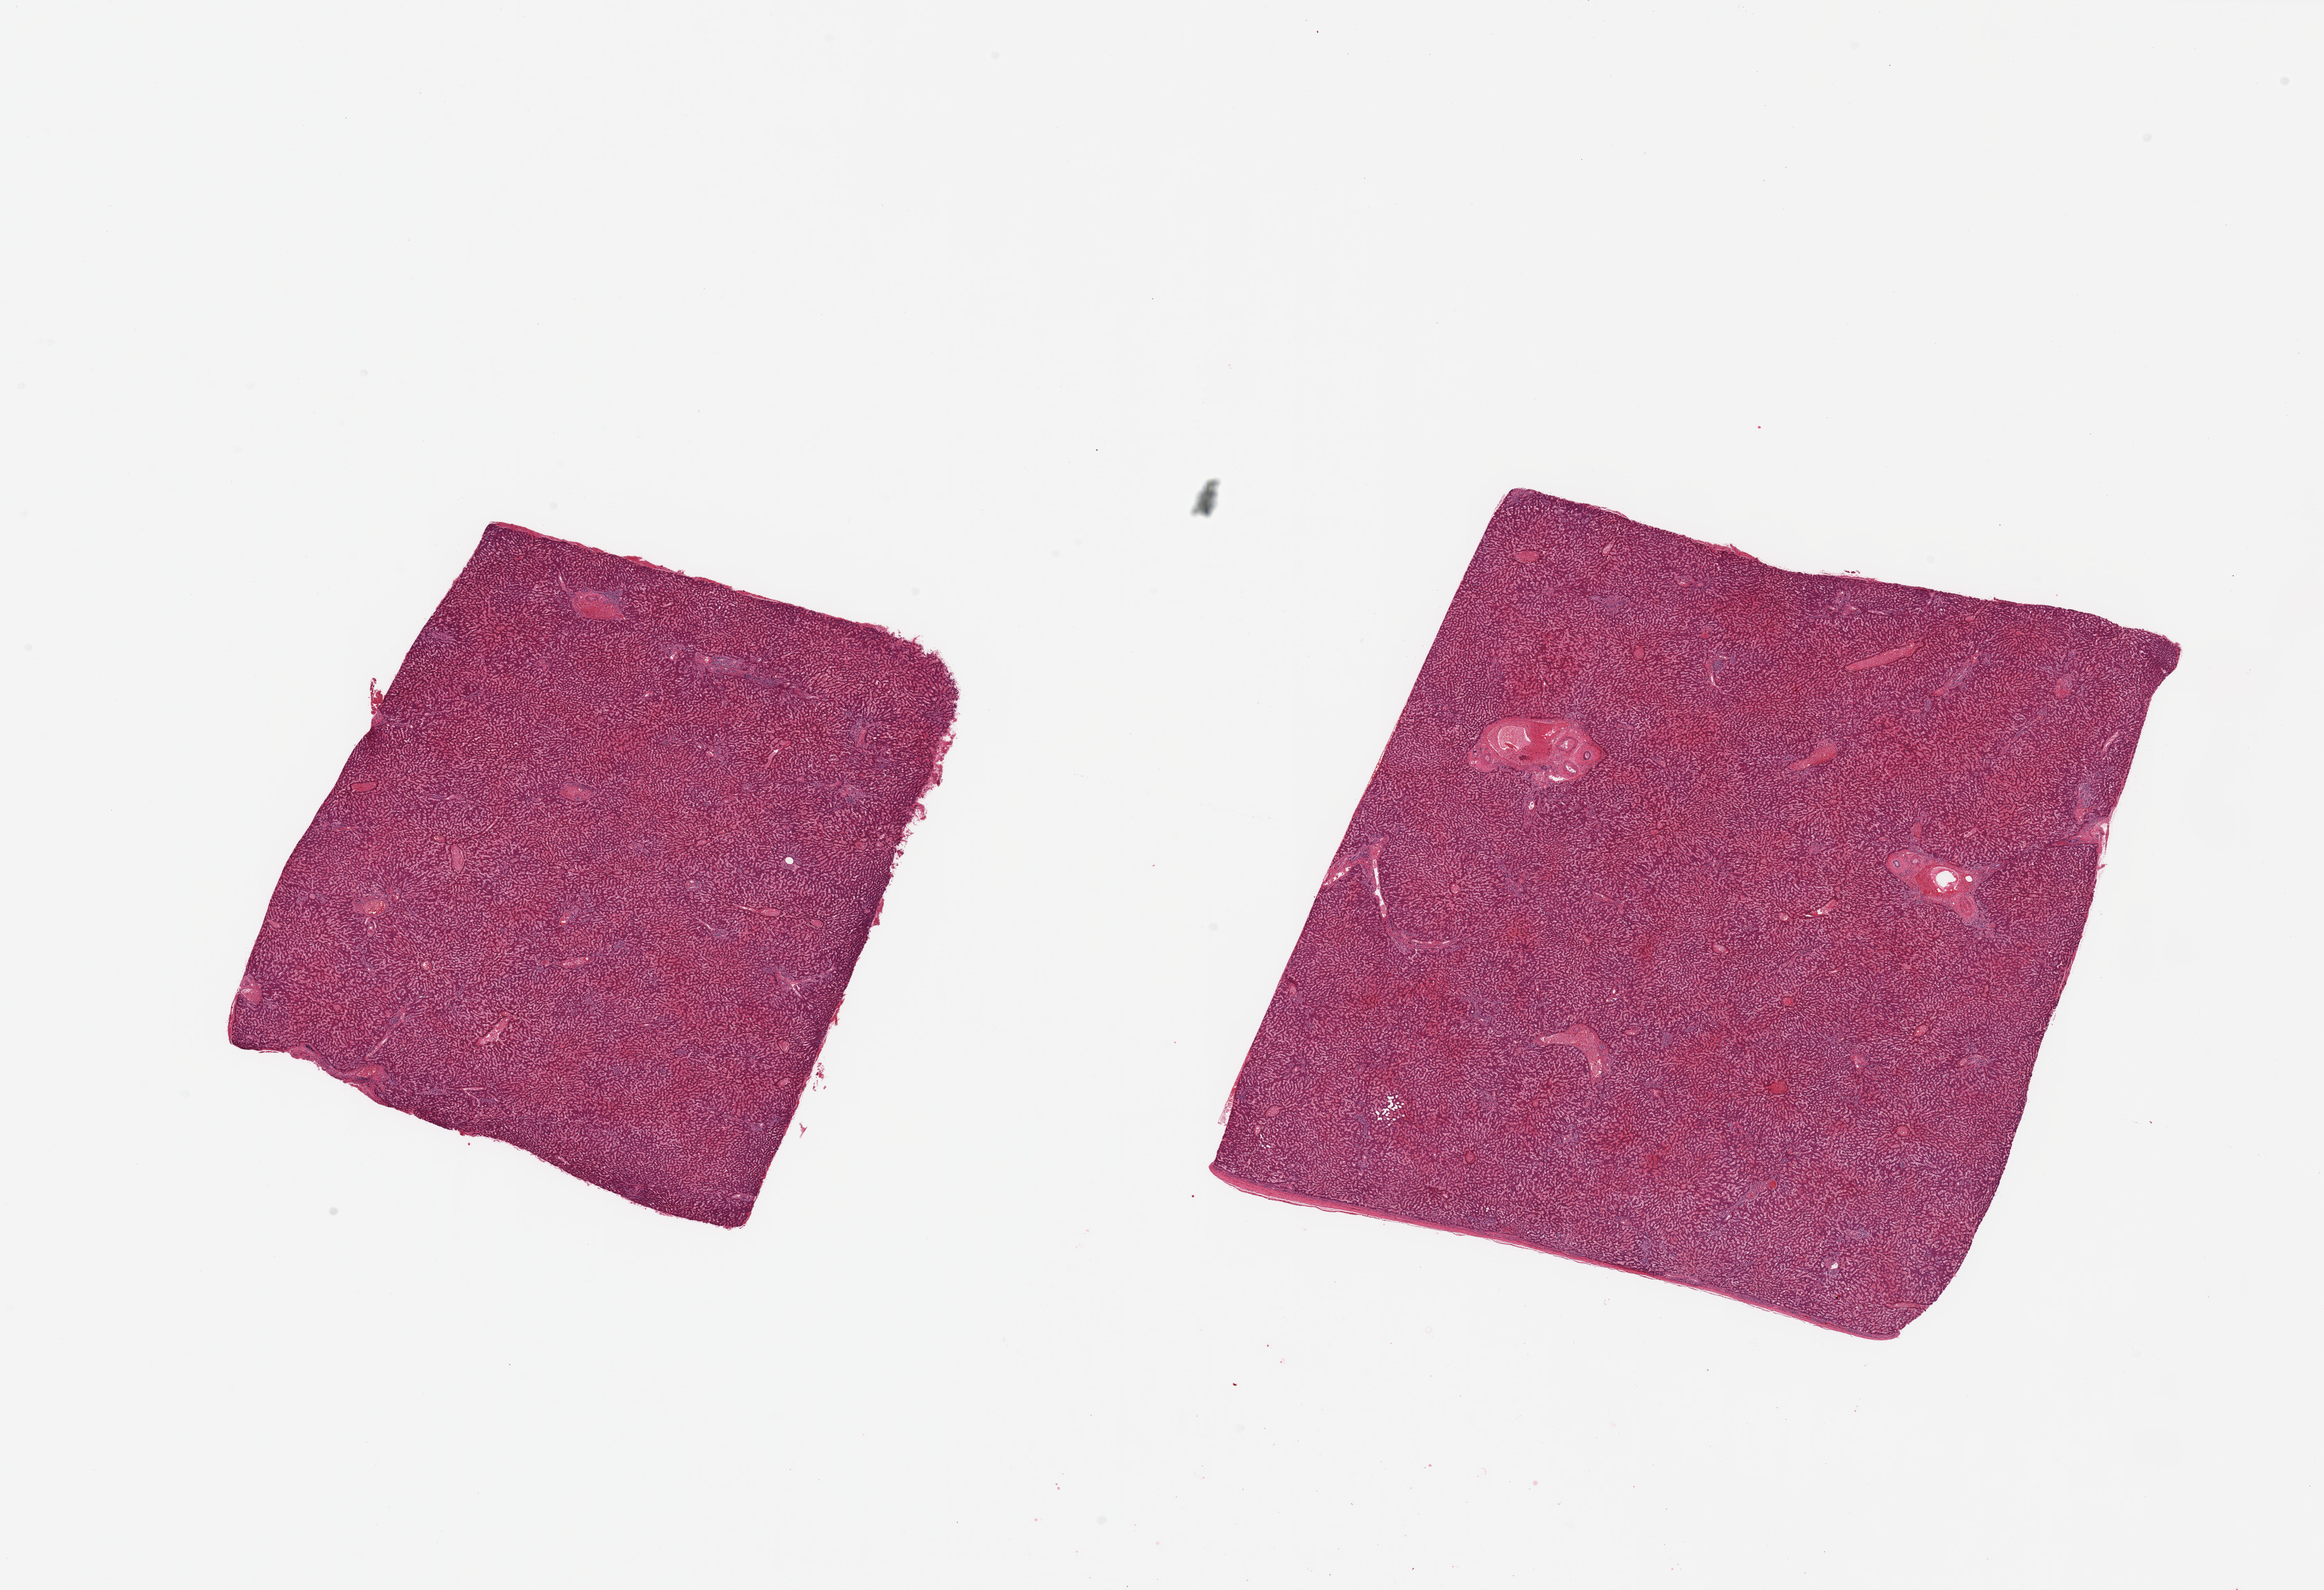
H&E whole-slide image, brightfield, low-resolution overview of the scanned area, about 26.6 x 18.2 mm. PAXgene-fixed paraffin-embedded (PFPE) section. Target tissue: liver. Tissue donor sample. Male donor.
- review note (as recorded): 2 pieces; marked congestion; one piece includes capsule